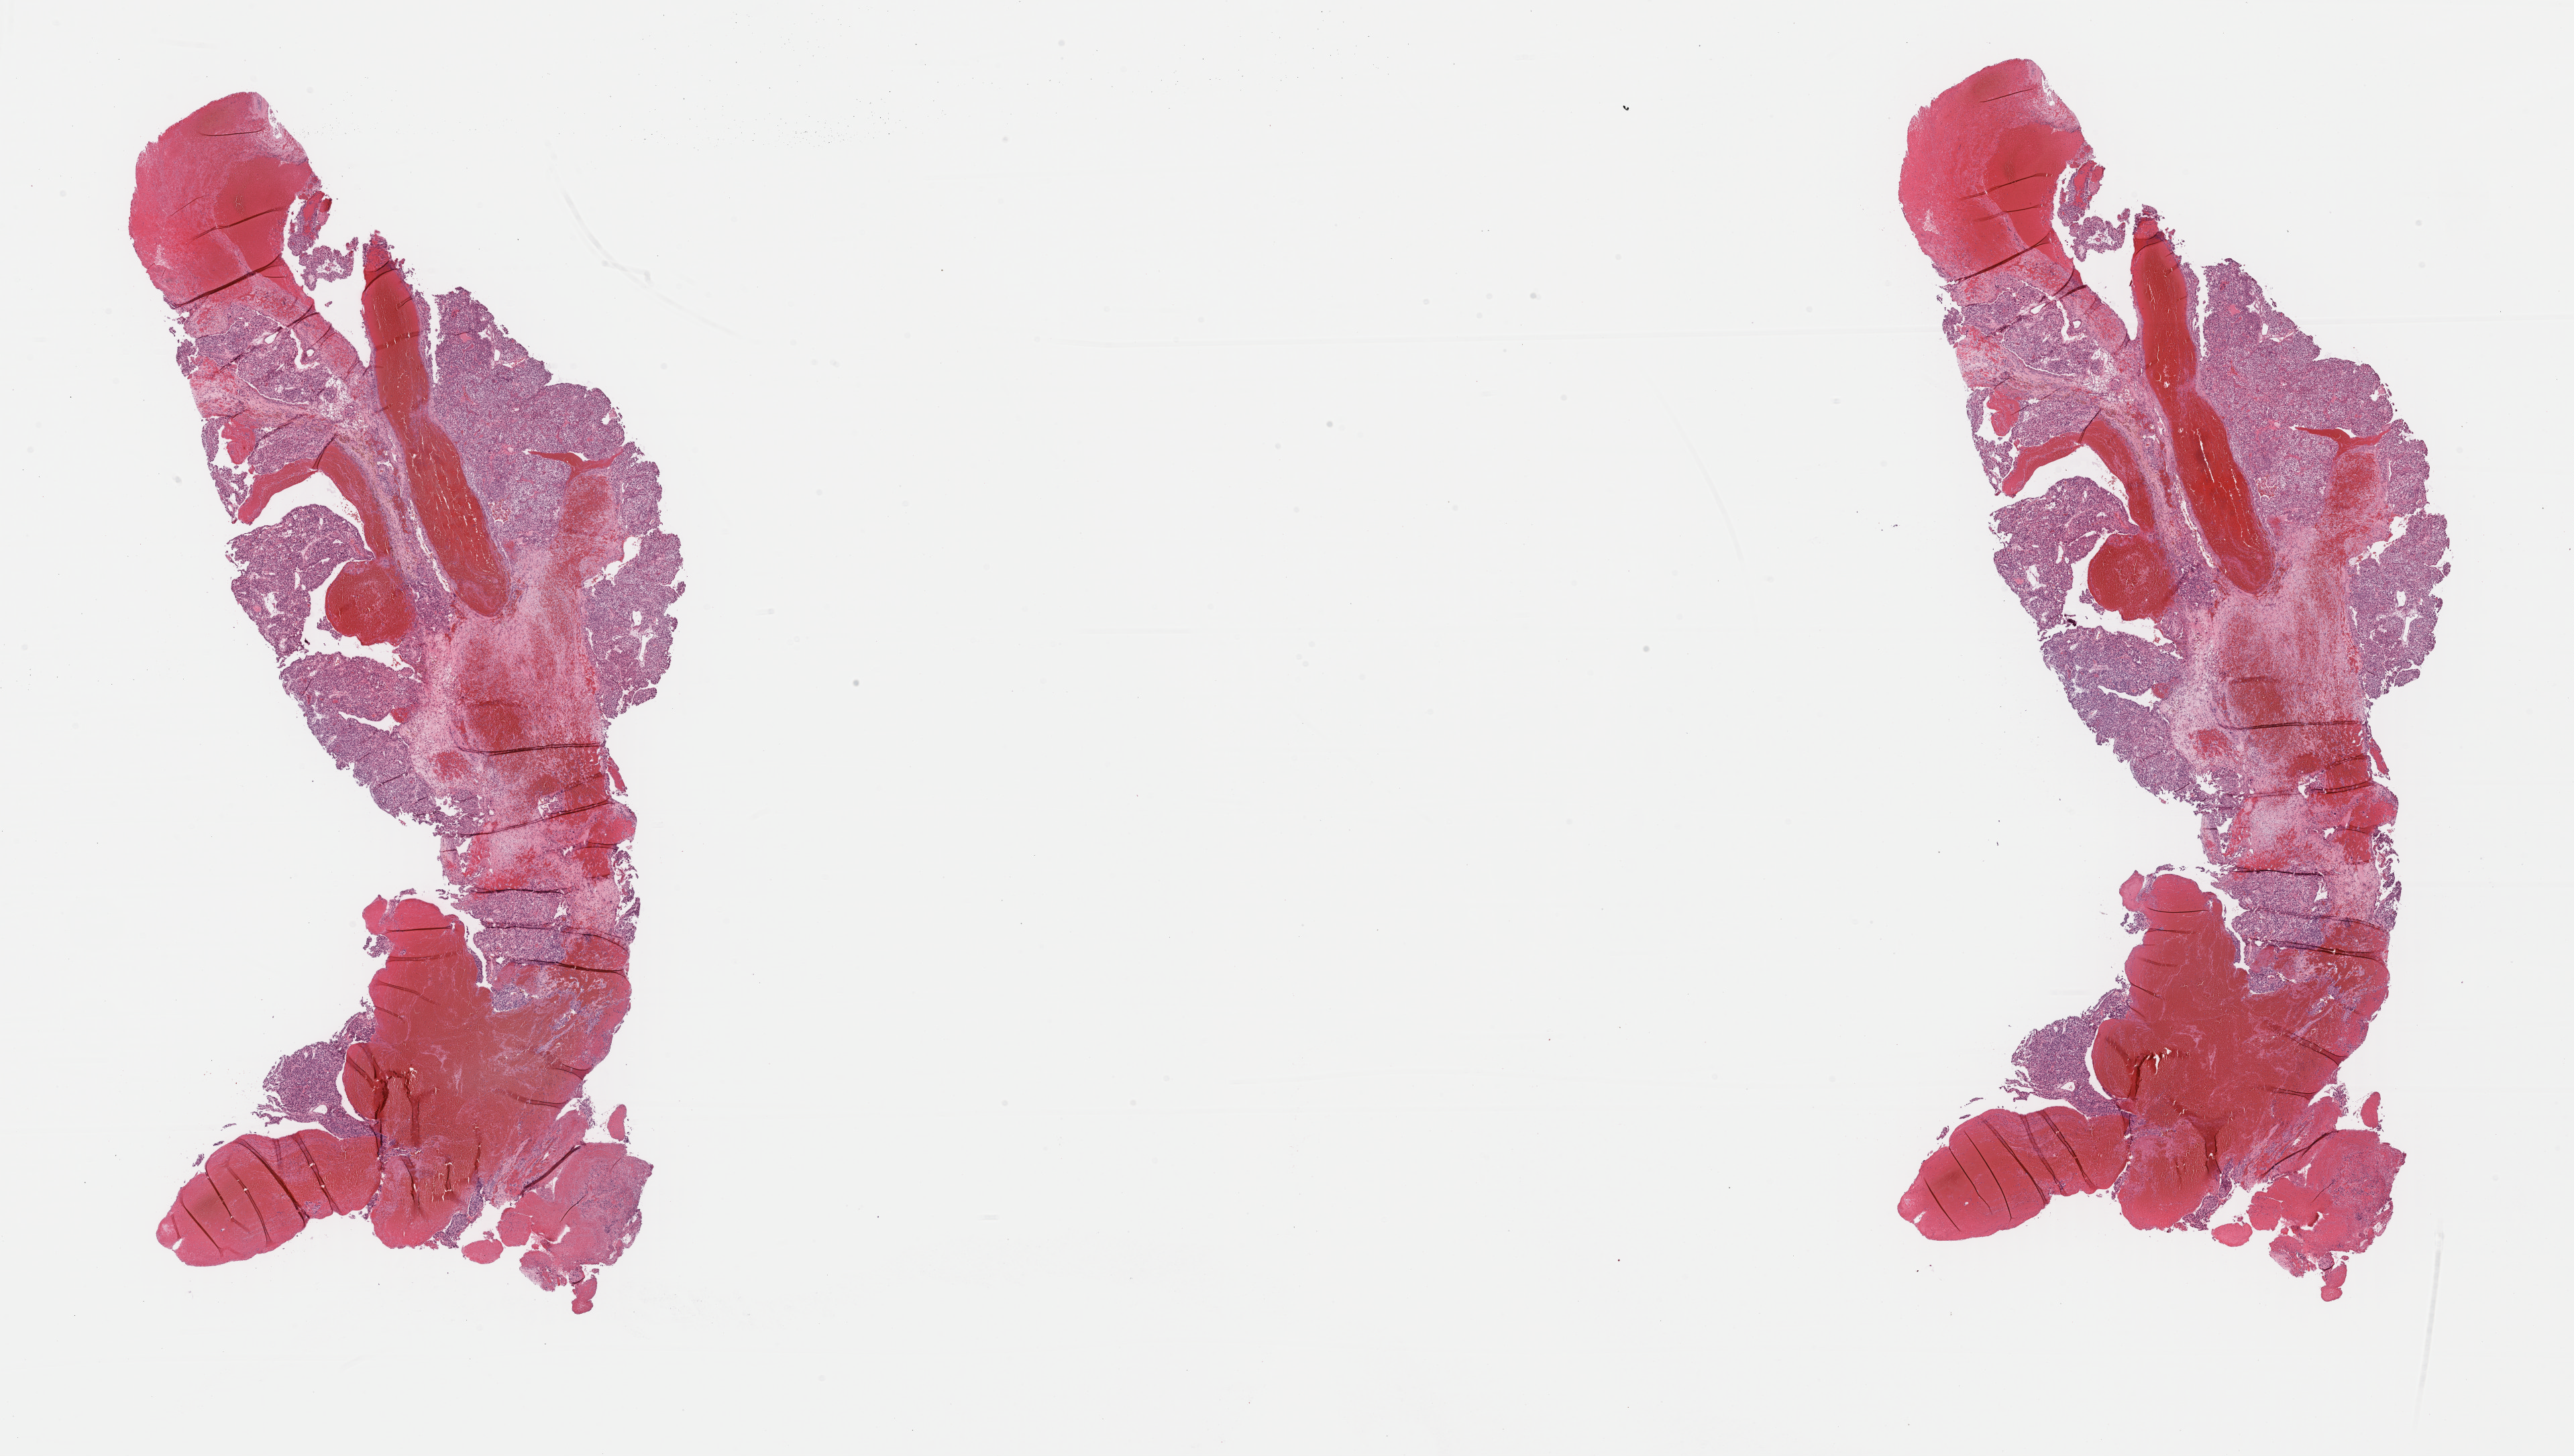
H&E whole-slide image — whole scanned area (about 30.3 x 17.1 mm) shown as a low-resolution overview, formalin-fixed paraffin-embedded (FFPE) diagnostic section, sample: primary tumour, bladder. Male patient; age at initial diagnosis 73 years.
Pathologic diagnosis: Transitional cell carcinoma (dome of bladder). AJCC pathologic stage: I.